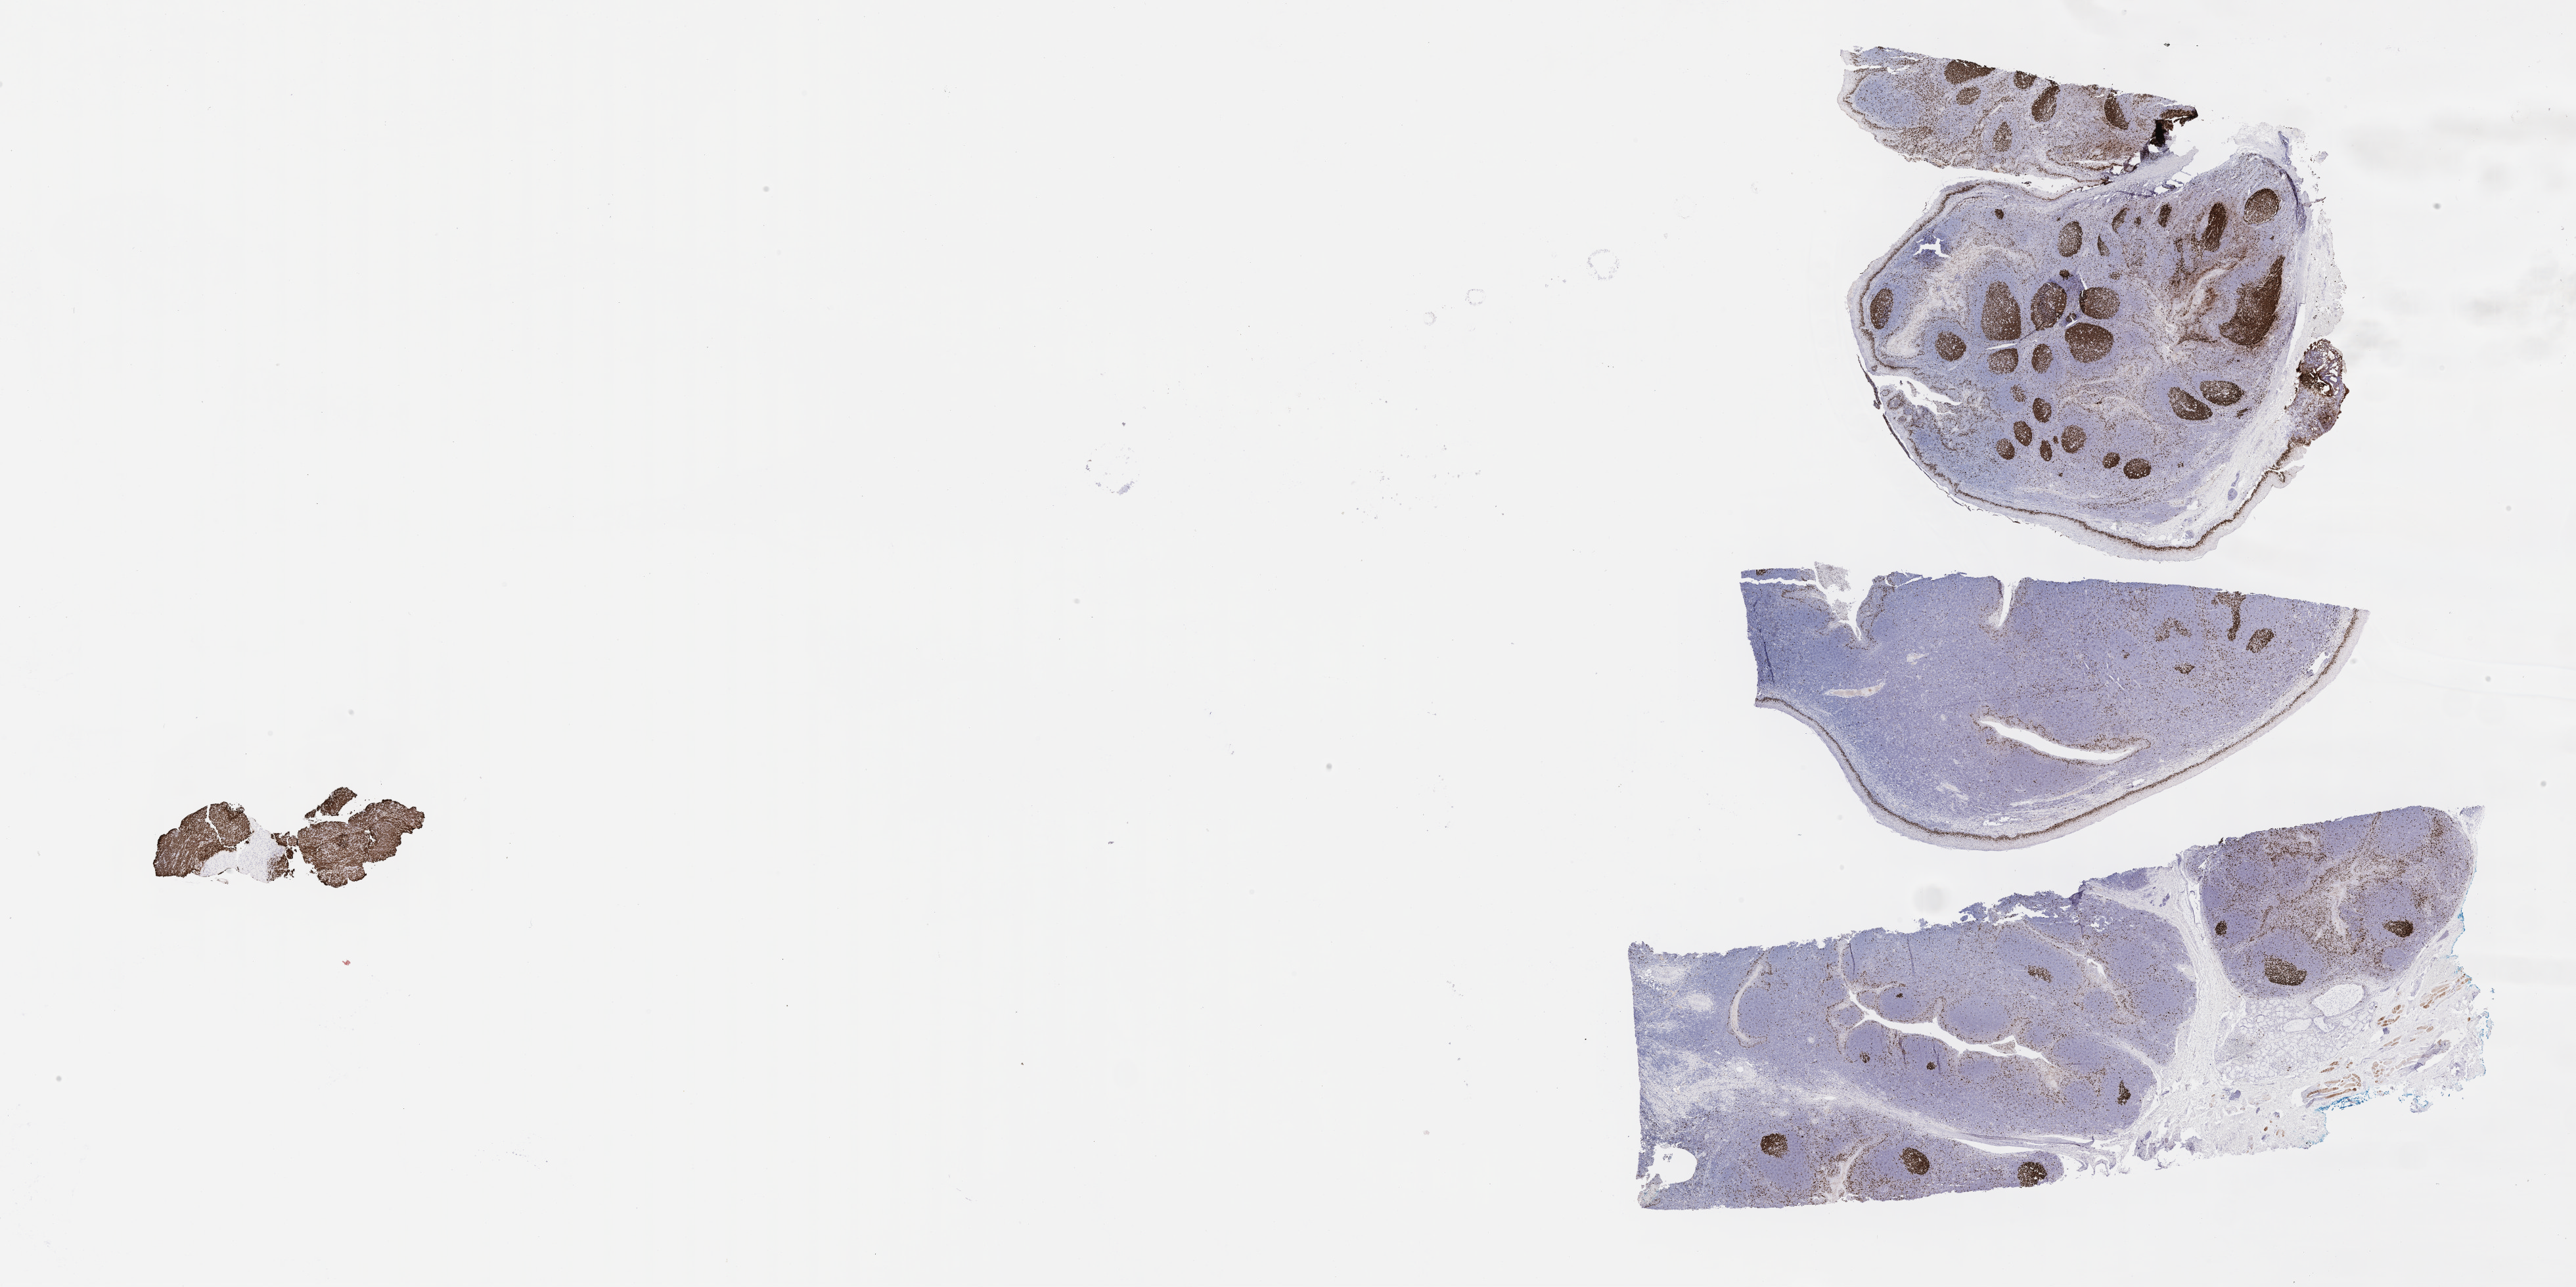
Whole-slide image, immunohistochemical stain for Ki-67, low-resolution overview of the scanned area, about 31.7 x 15.8 mm. Tumor tissue. Male patient, aged 15.
Diagnosis: Burkitt lymphoma, NOS.